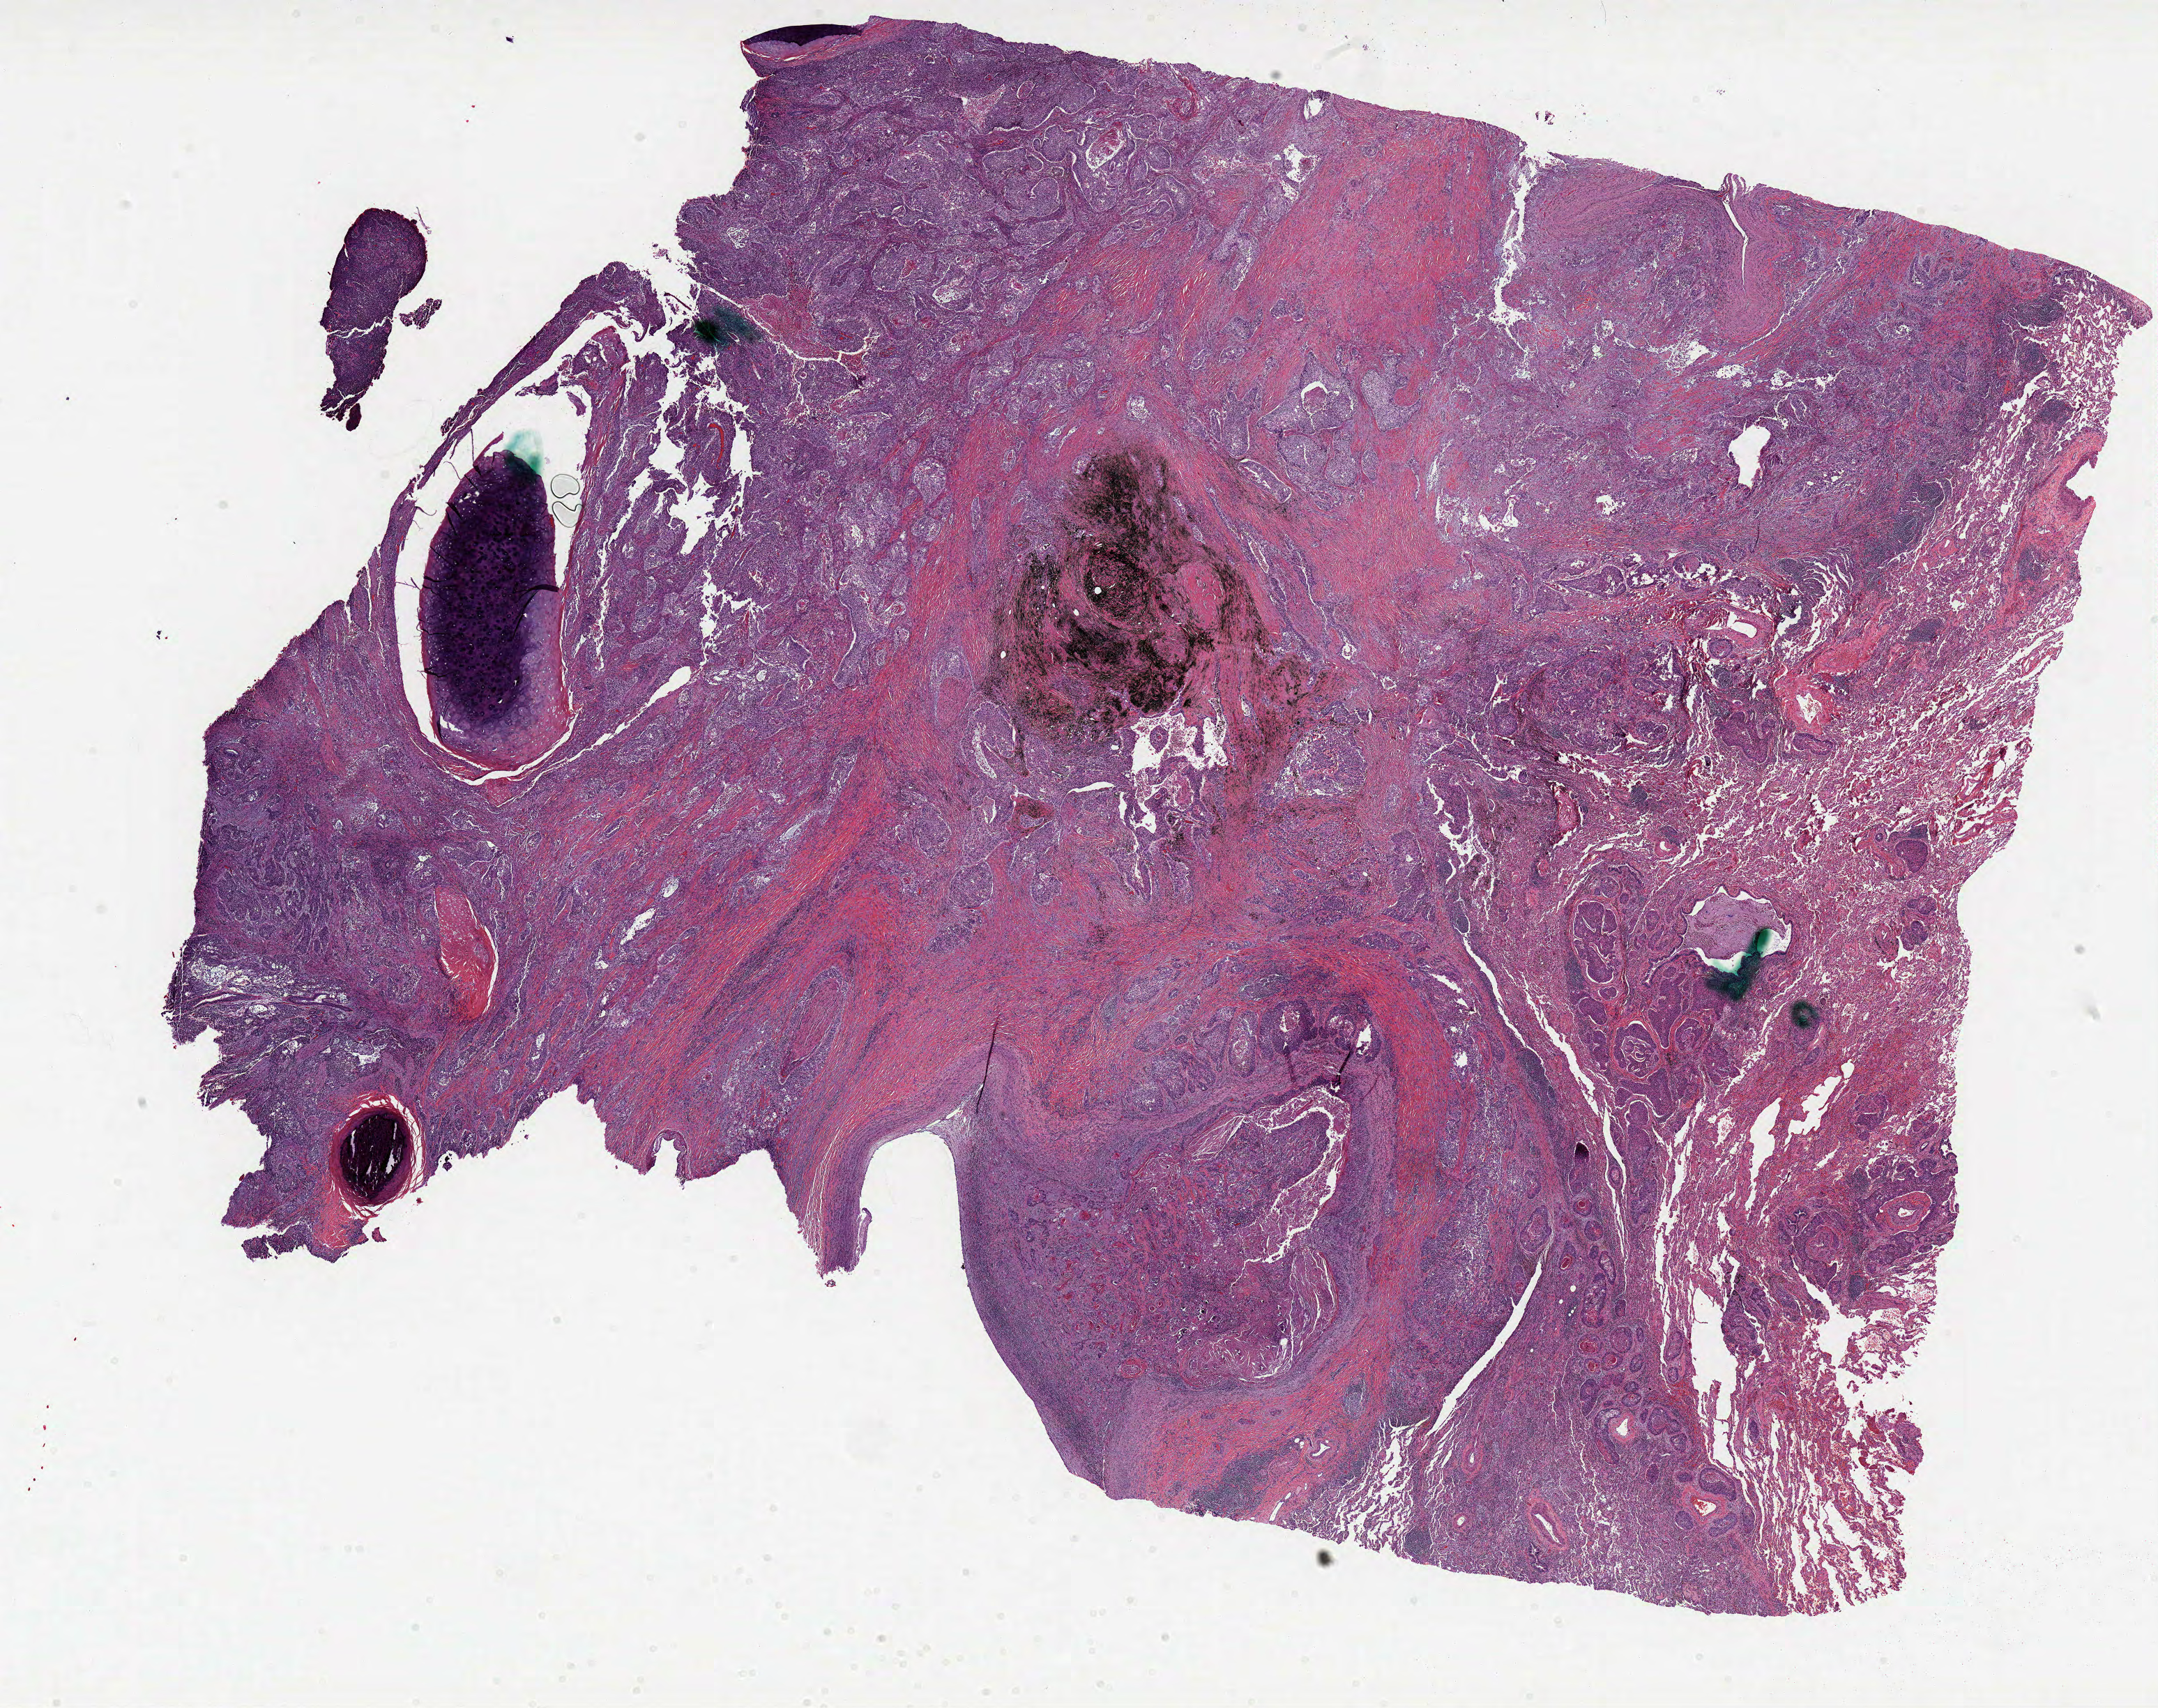
Whole-slide histology image, Hematoxylin and eosin (H&E) stained — whole scanned area (about 25.0 x 19.8 mm, from a 20x scan) shown as a low-resolution overview; FFPE section; primary tumour sample from the lung. Patient: male, age at initial diagnosis 67 years.
* laterality: left
* pathologic diagnosis: Squamous cell carcinoma, NOS (lower lobe, lung)
* AJCC pathologic stage: IIIA